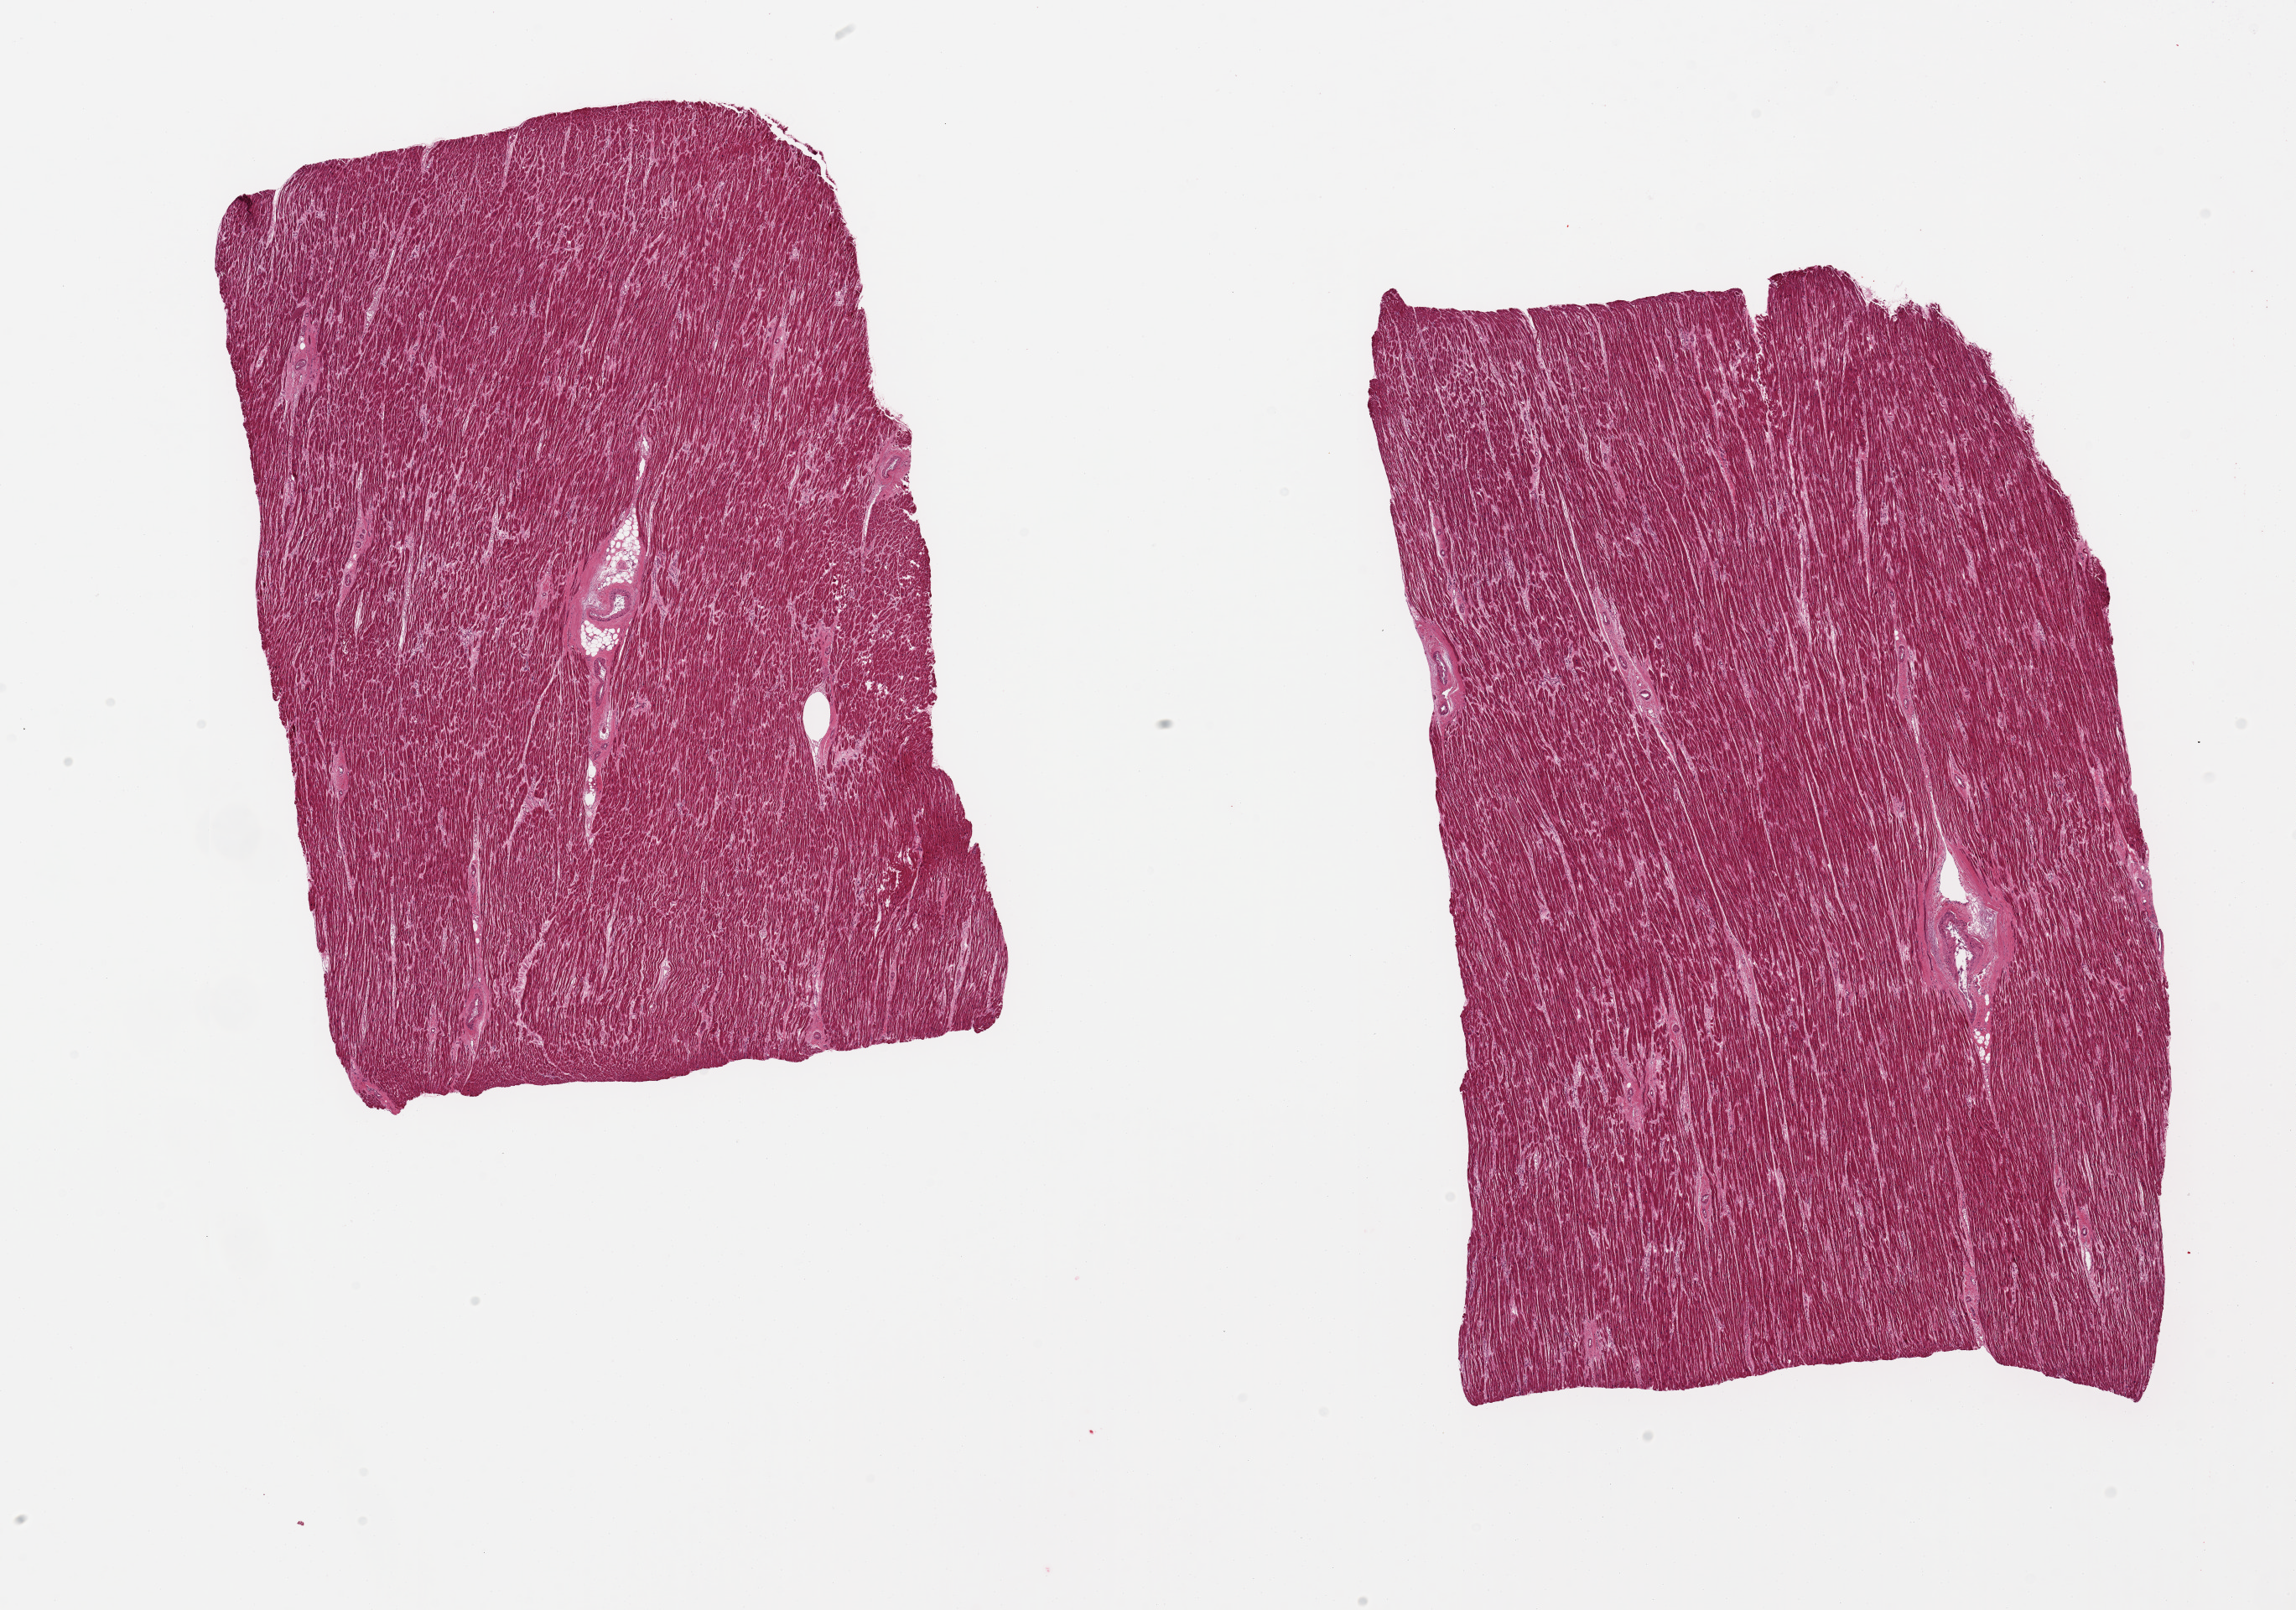
Whole-slide image, haematoxylin and eosin stain — whole scanned area (about 21.7 x 15.2 mm) shown as a low-resolution overview. PAXgene-fixed paraffin-embedded (PFPE) section. Section of heart (target tissue). Donor tissue sample.
• review note (as recorded): 2 pieces, moderate chronic ischemic changes/interstitial fibrosis, remote microinfarcts